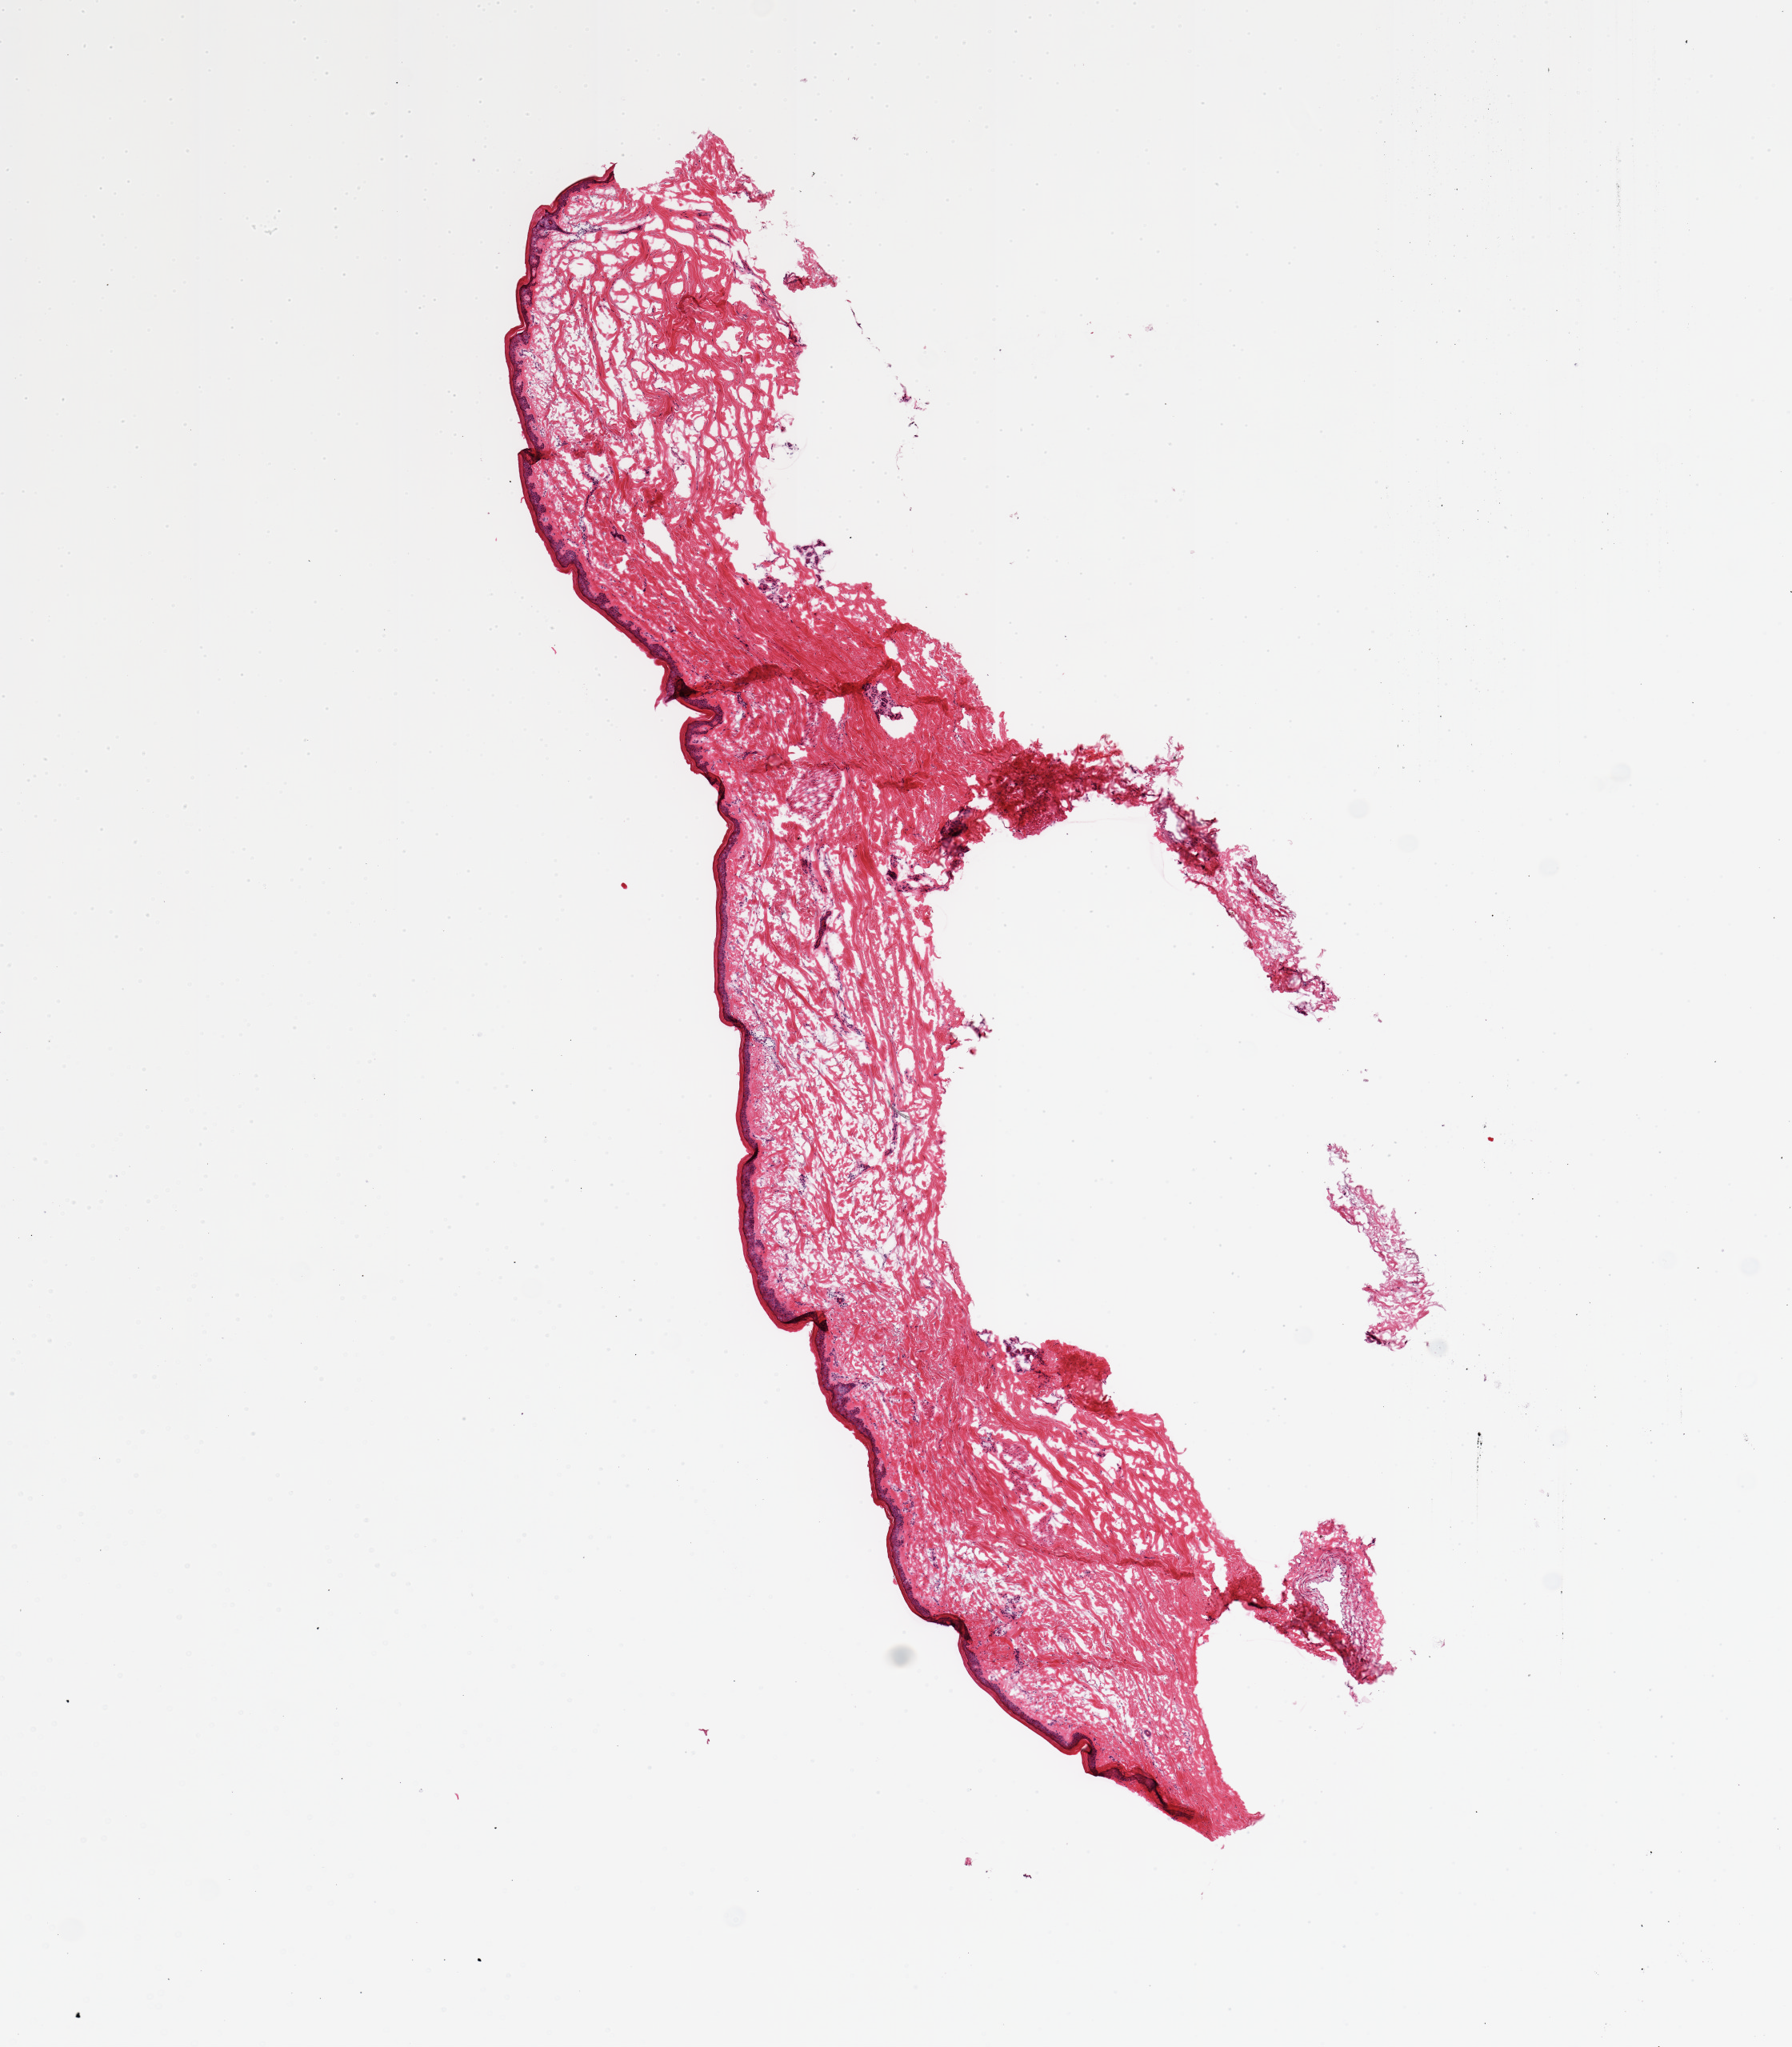
Digitized hematoxylin and eosin (H&E)-stained section — low-resolution overview of the scanned area, about 8.9 x 10.1 mm (slide scanned at 20x). Frozen section (dry ice). Sampled site (target tissue): skin of lower leg. Tissue donor sample. Donor: female.
Pathologist's review note for this sample: 1 piece.